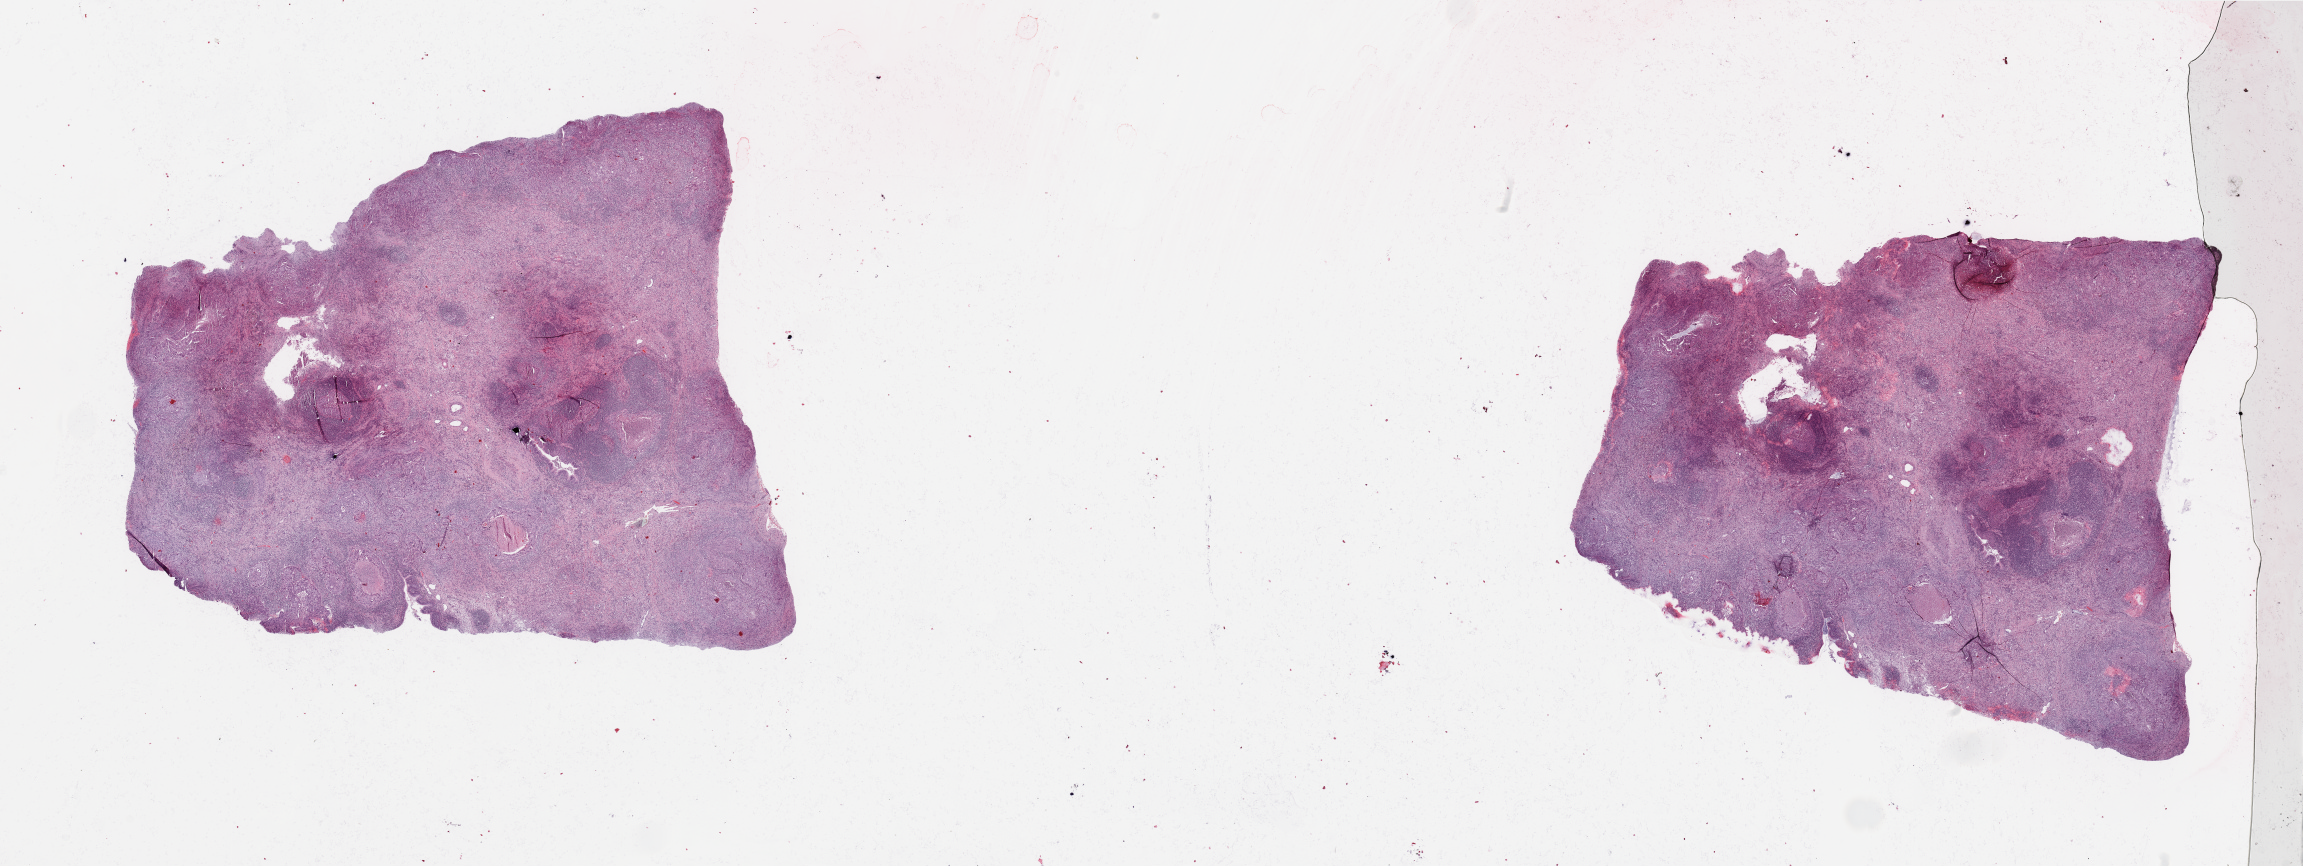
Digitized Hematoxylin and eosin (H&E) stained tissue section (whole slide) — whole scanned area (about 36.4 x 13.7 mm, acquisition: 20x scan) shown as a low-resolution overview; lung, tumour tissue. Patient: male, age 57 years. Histologic grade: G2 (moderately differentiated).
AJCC pathologic stage: IIB. Primary tumour site (as recorded): right lower lobe. Diagnosis: Squamous cell carcinoma, NOS.